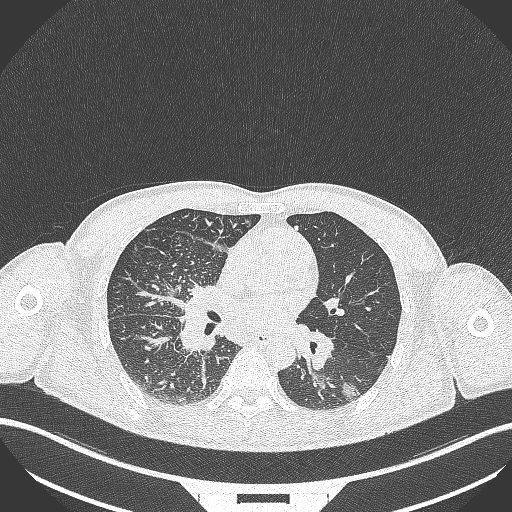
Chest CT, one axial slice; lung window (W 1500 / L -600 HU); 1 mm slice thickness; 512 × 512 image matrix, field of view 400 × 400 mm. Male patient, age 49 years. From the clinical record (not read from this slice): clinical TNM (as recorded): T2b N1 M0.
Annotated regions visible in this slice (bounding box drawn by a radiologist):
- lung tumour (recorded histology: adenocarcinoma): bounding box <308,370,359,401> (left, top, right, bottom; pixels)